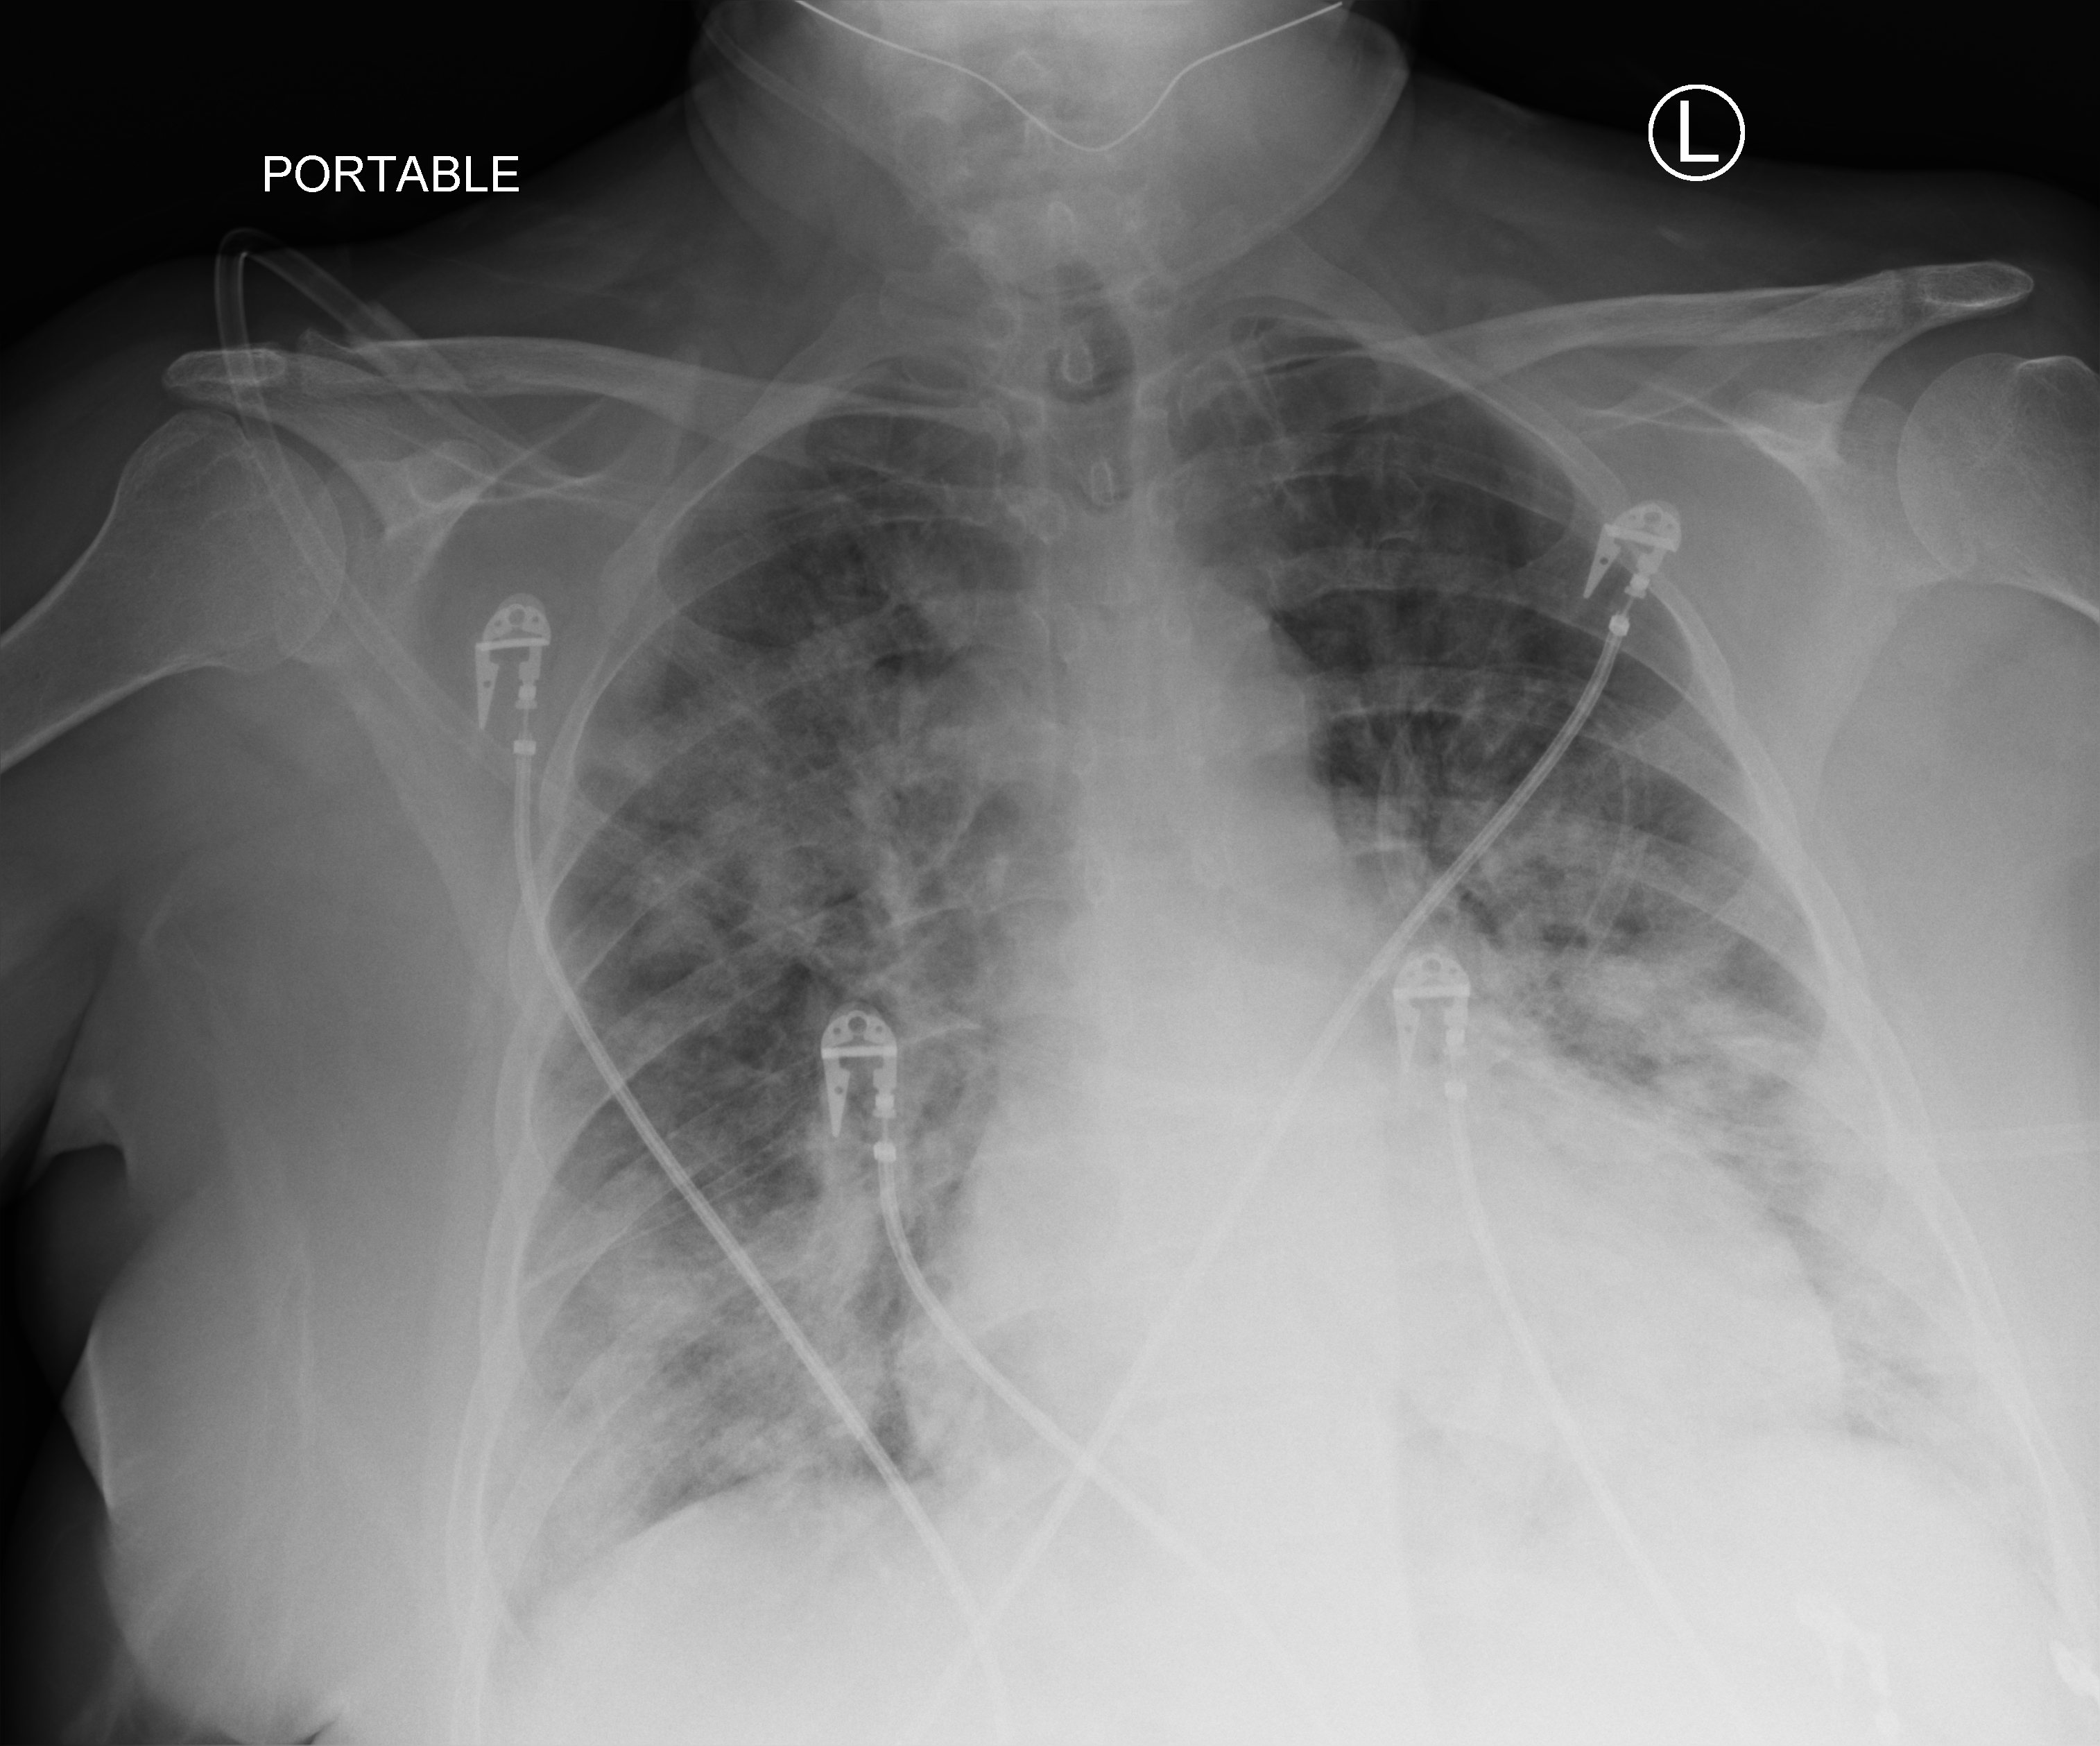
Chest X-ray (portable), anteroposterior (AP) projection. Patient hospitalised with COVID-19; female, aged 60–74 years.
Admission-level facts for this patient (not findings on this image; timing relative to this image not recorded): diabetes (admission record): yes; length of hospital stay: 17 days; mechanically ventilated during this hospital stay: no.